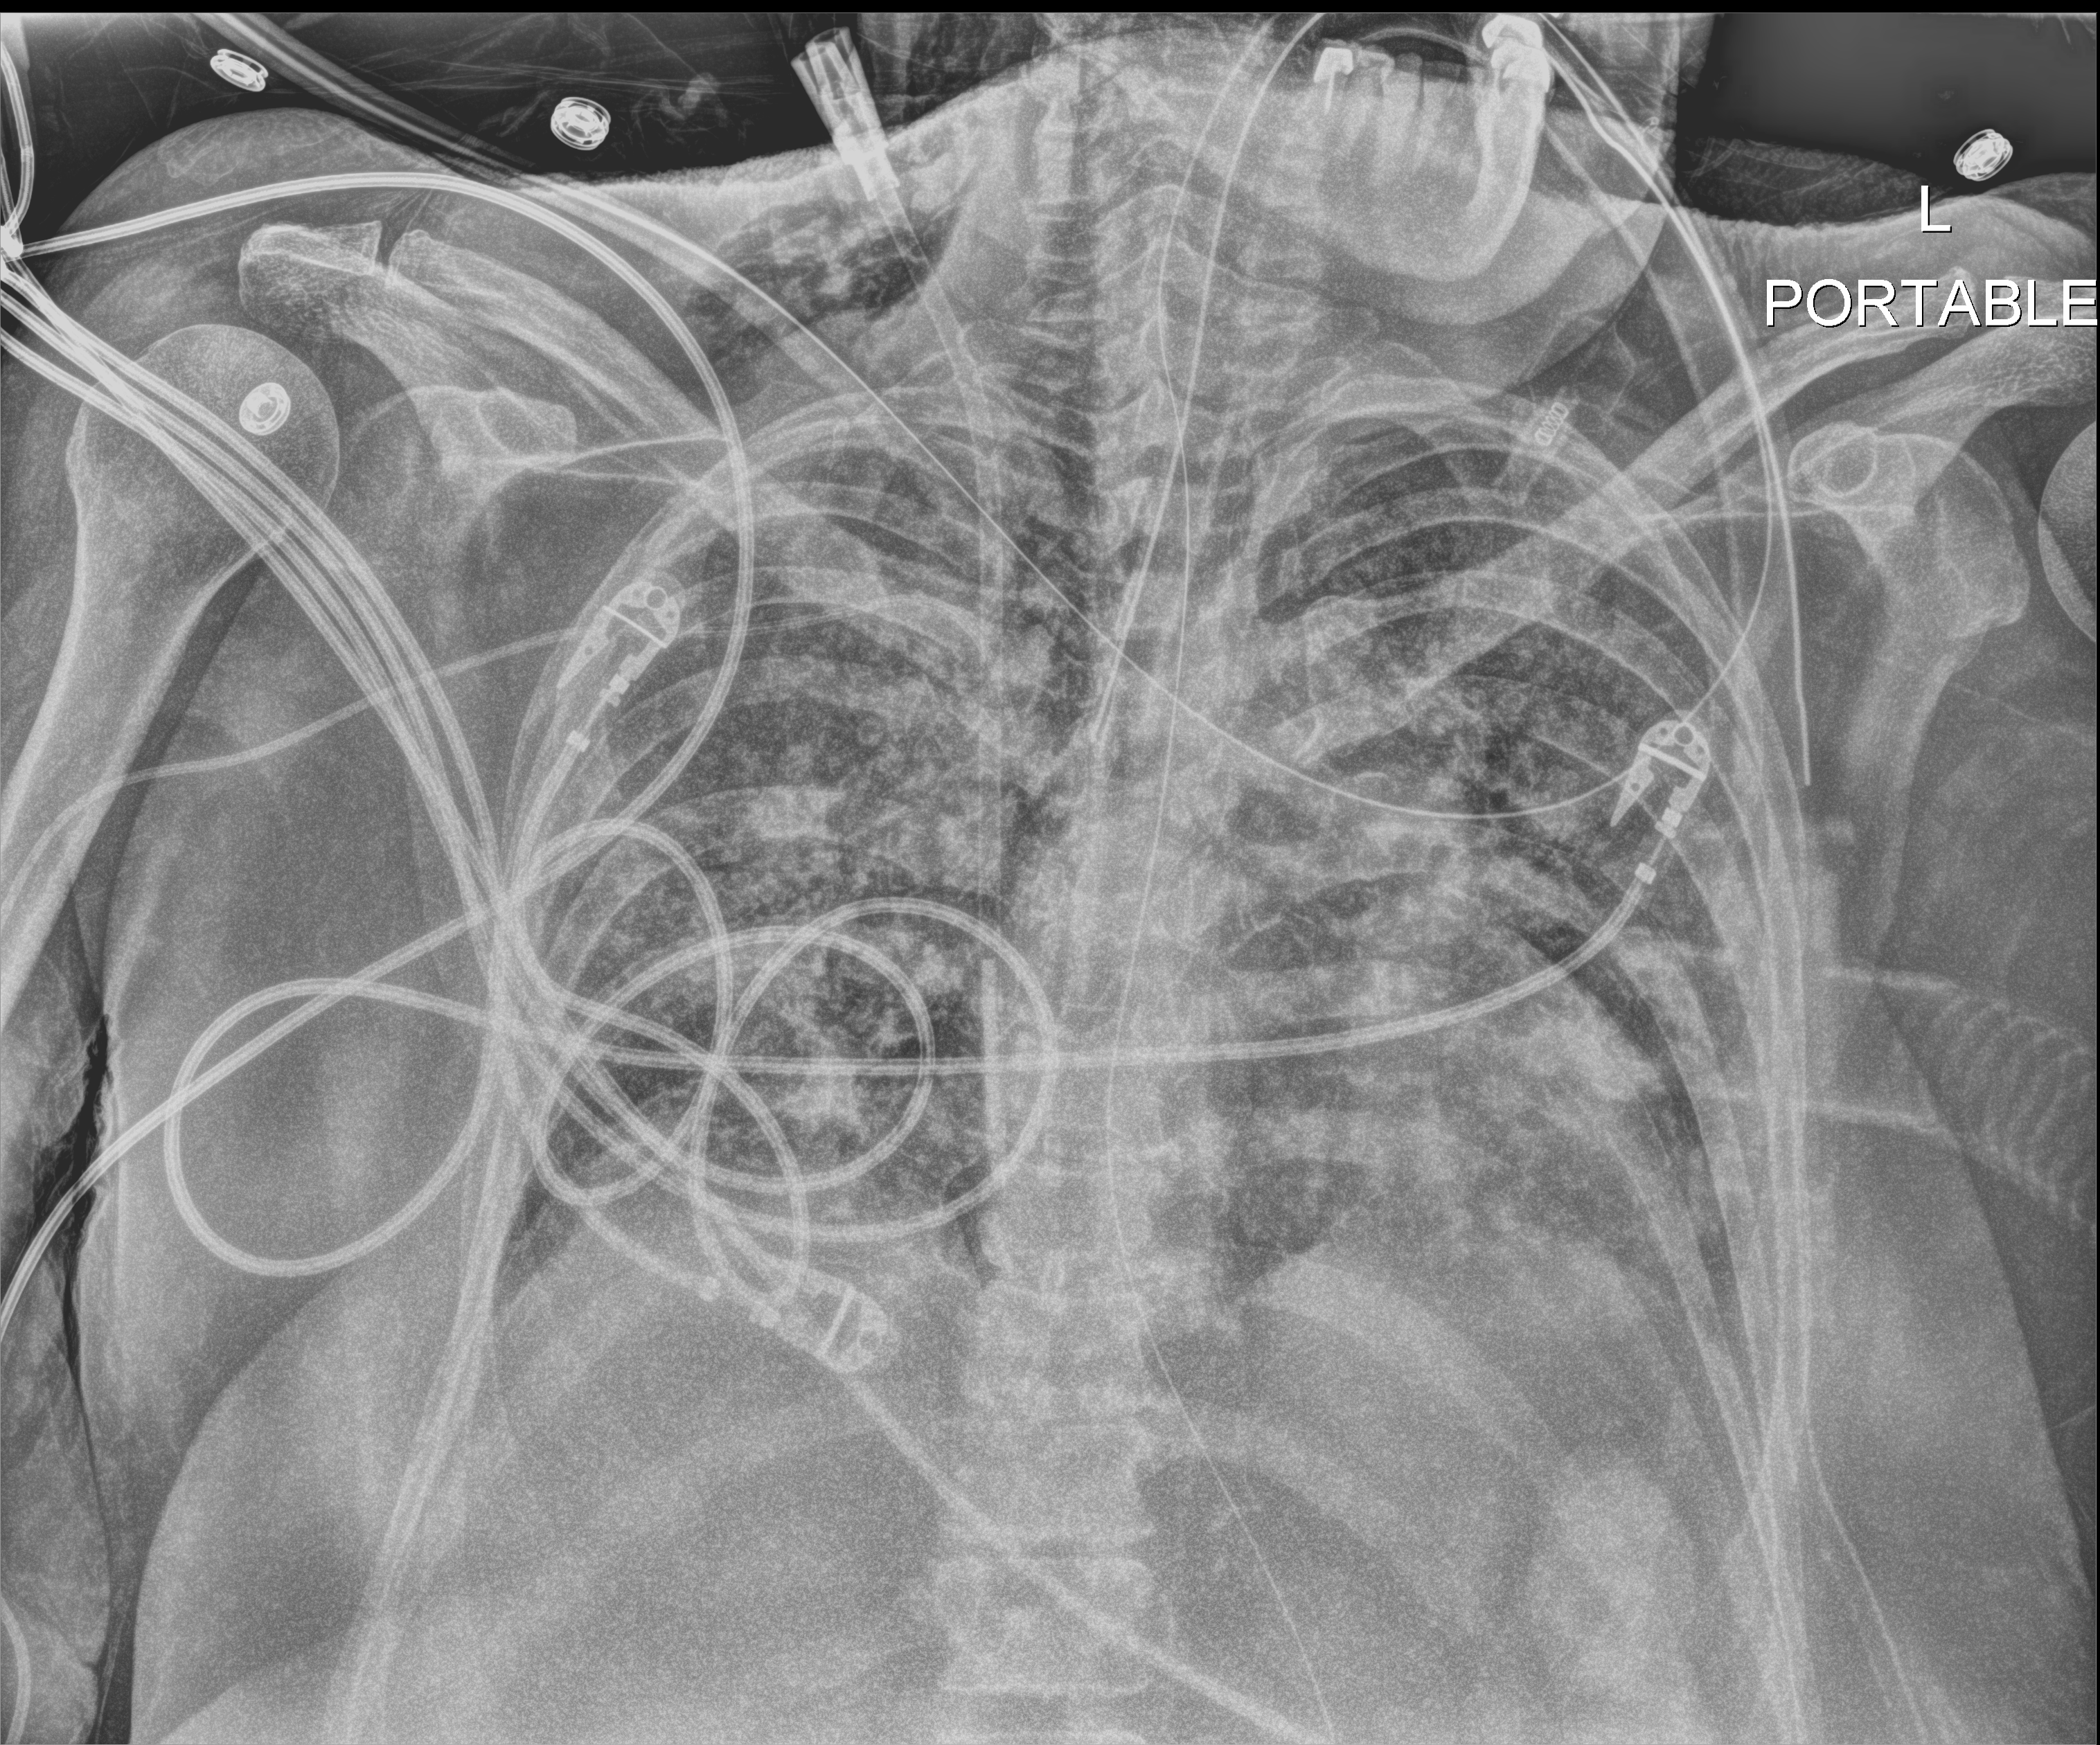
Chest radiograph. Patient hospitalised with COVID-19; female, aged 60–74 years.
Hospital-stay facts (about this admission, not read from this image; timing relative to this image not recorded):
- admitted to intensive care during this hospital stay: yes
- smoking status (admission record): never